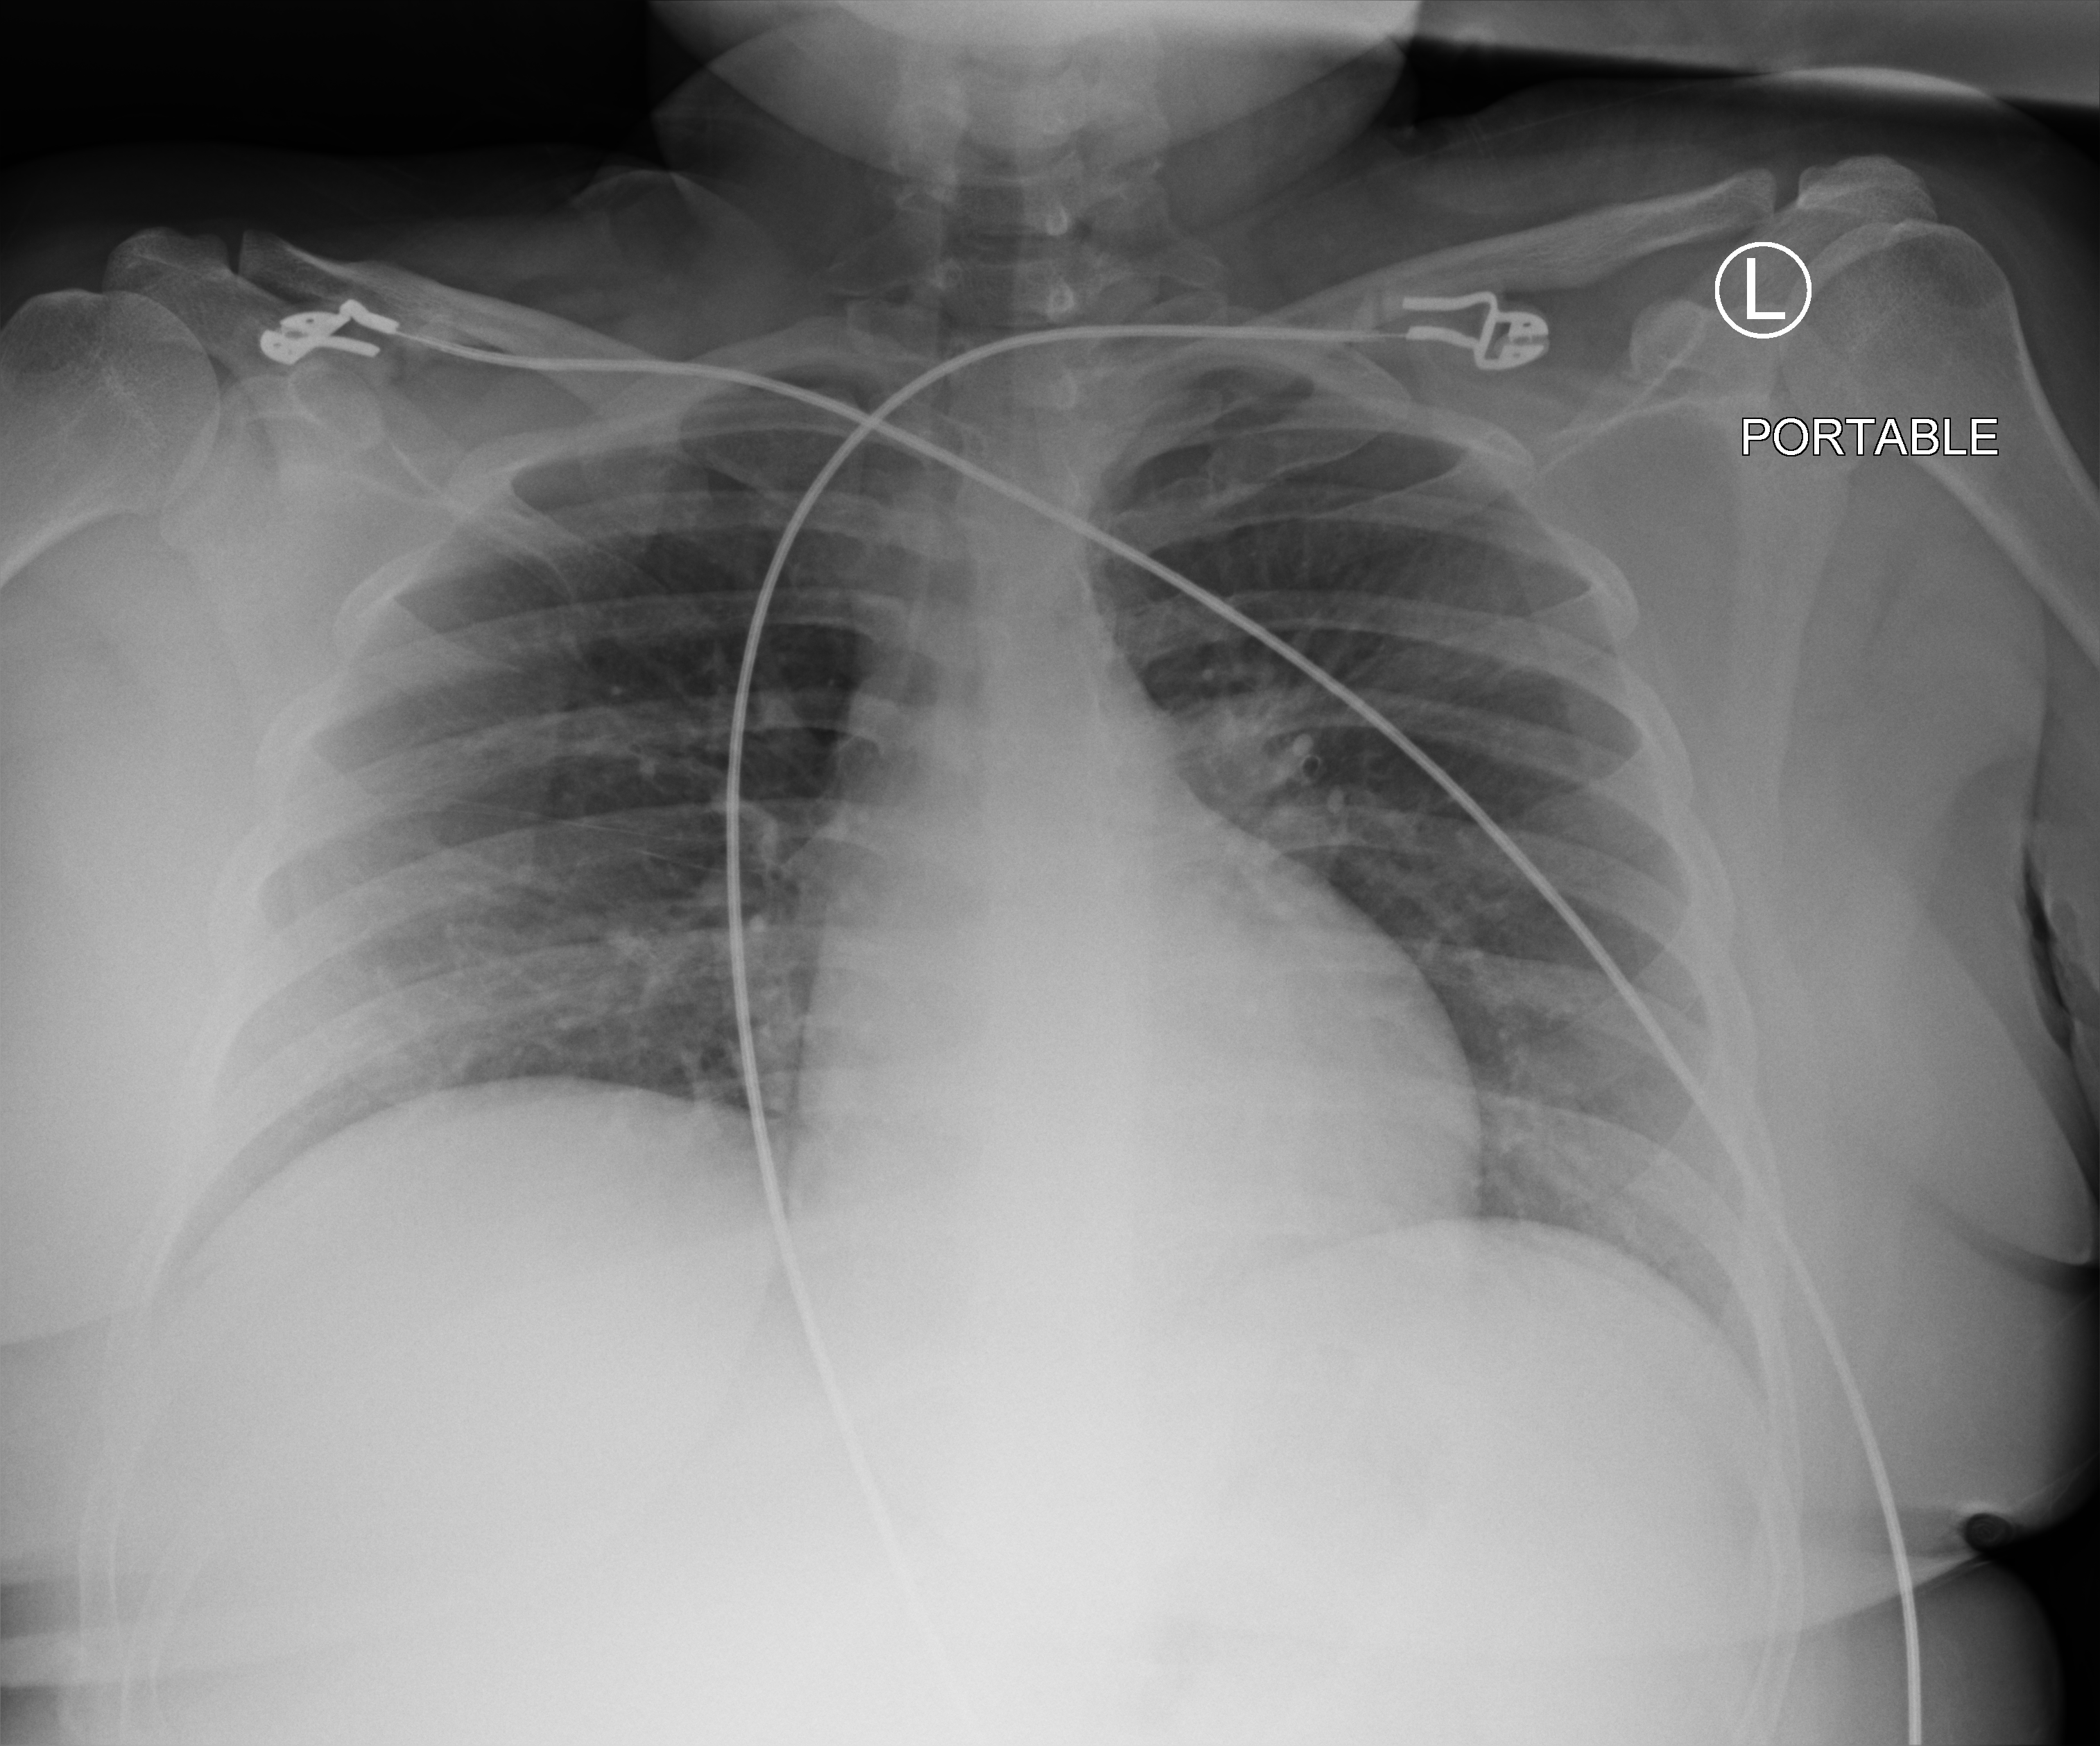
Chest X-ray (portable), anteroposterior (AP) projection. Female patient hospitalised with COVID-19, age 18–59 years.
Hospital-stay facts (about this admission, not read from this image; timing relative to this image not recorded): mechanically ventilated during this hospital stay: no.